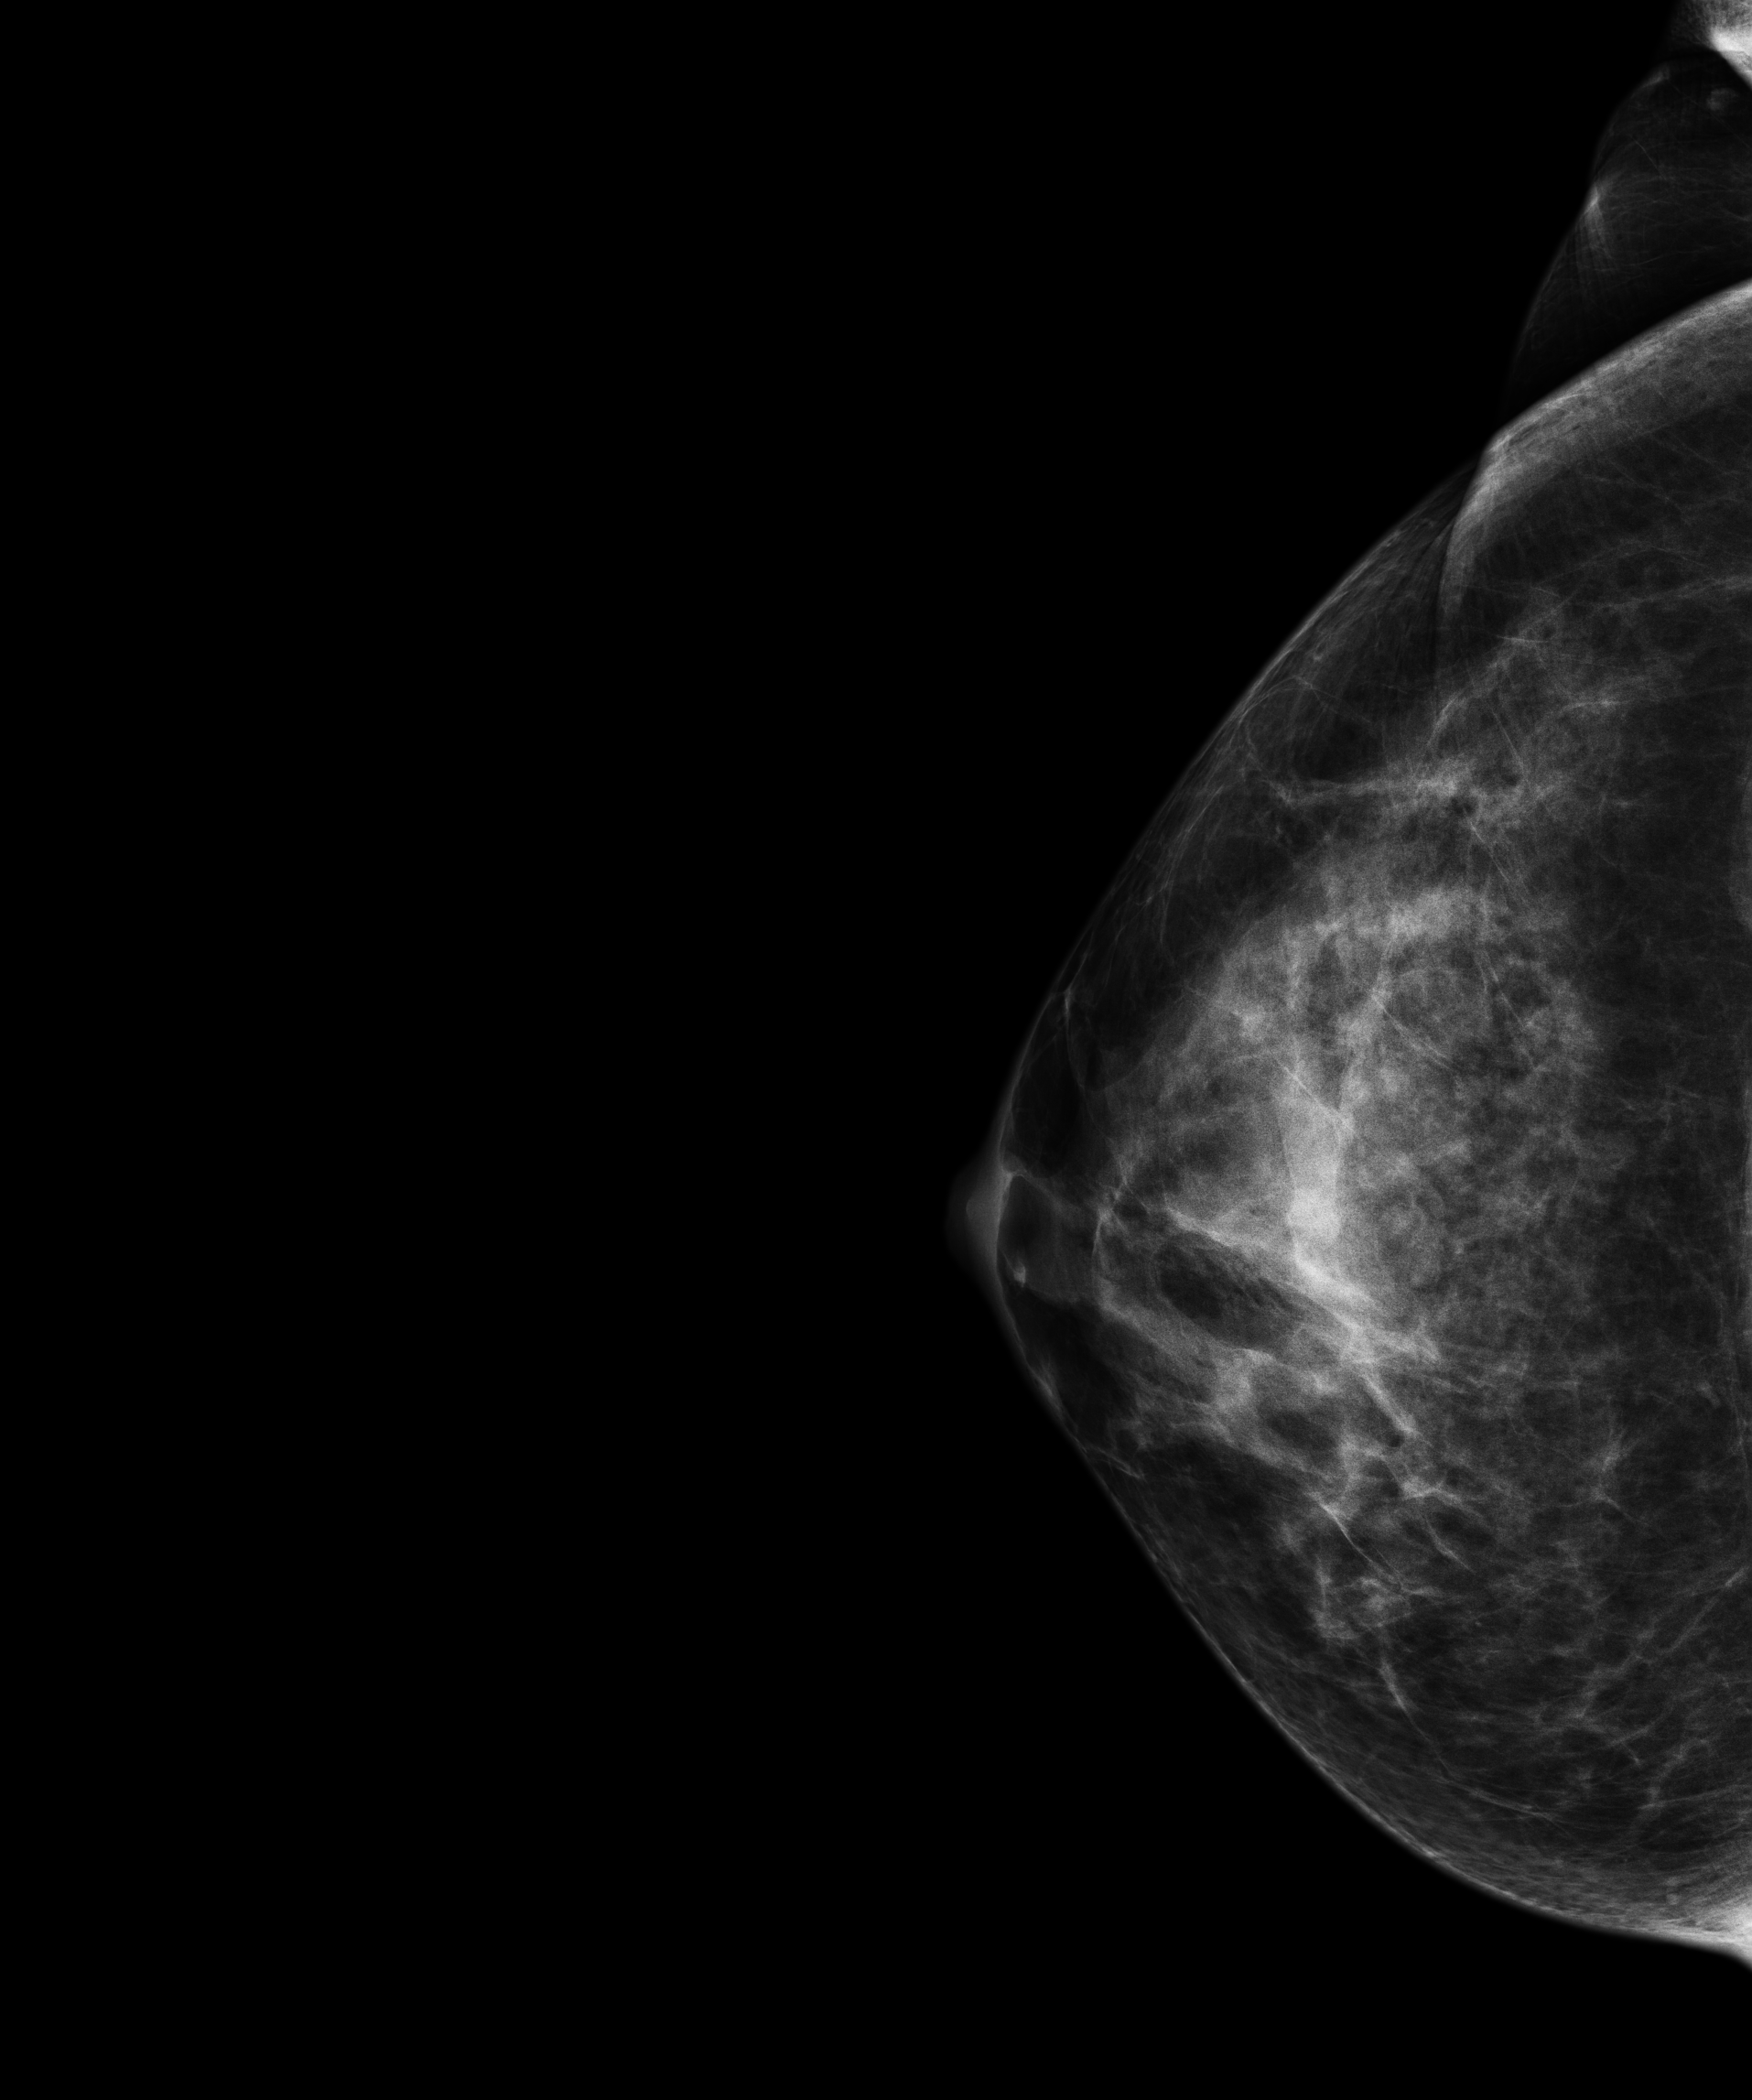
Full-field digital mammogram (FFDM); right breast; craniocaudal (CC) view; annual screening mammography examination; compressed breast thickness 61 mm. Female patient, age 42 years.
- BI-RADS breast density category at the screening exam (both breasts, scale 1–4): 3
- final BI-RADS assessment for this screening round (tomosynthesis exam, both breasts): category 1
- recall: no recall after this screen